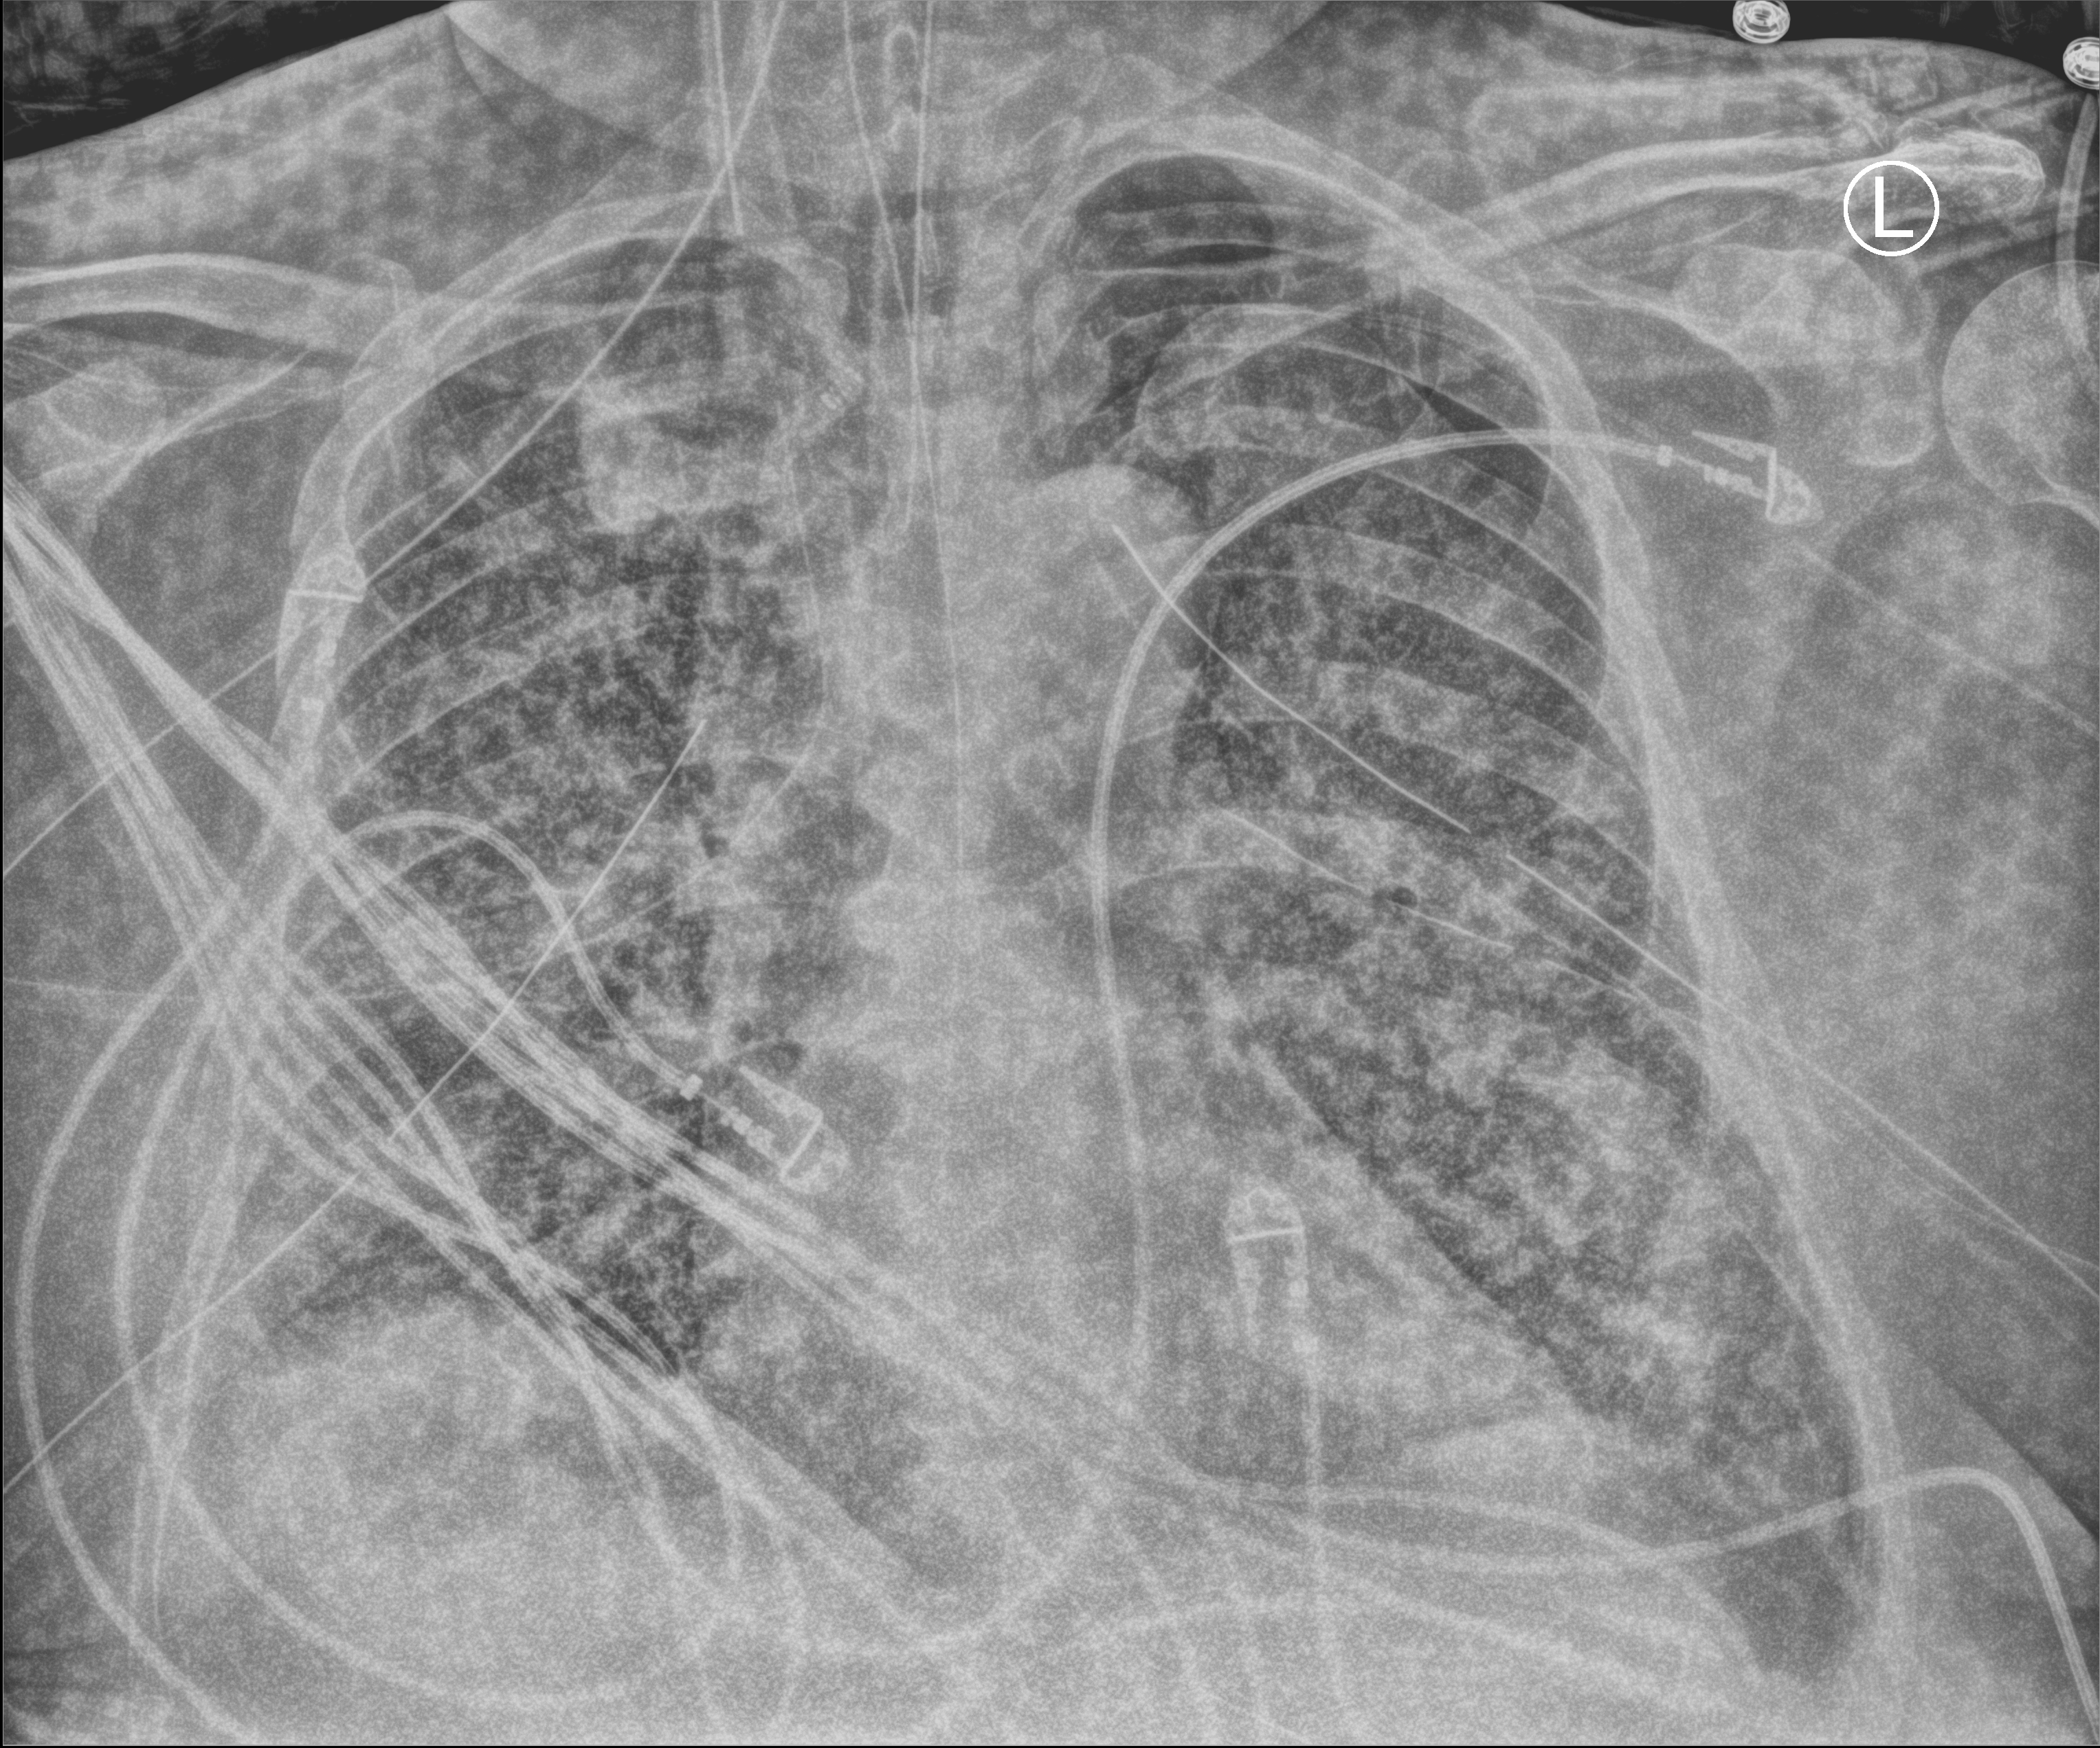
Chest X-ray (portable). Patient hospitalised with COVID-19, aged 18–59 years.
Hospital-stay facts (about this admission, not read from this image; timing relative to this image not recorded): mechanically ventilated during this hospital stay: yes.